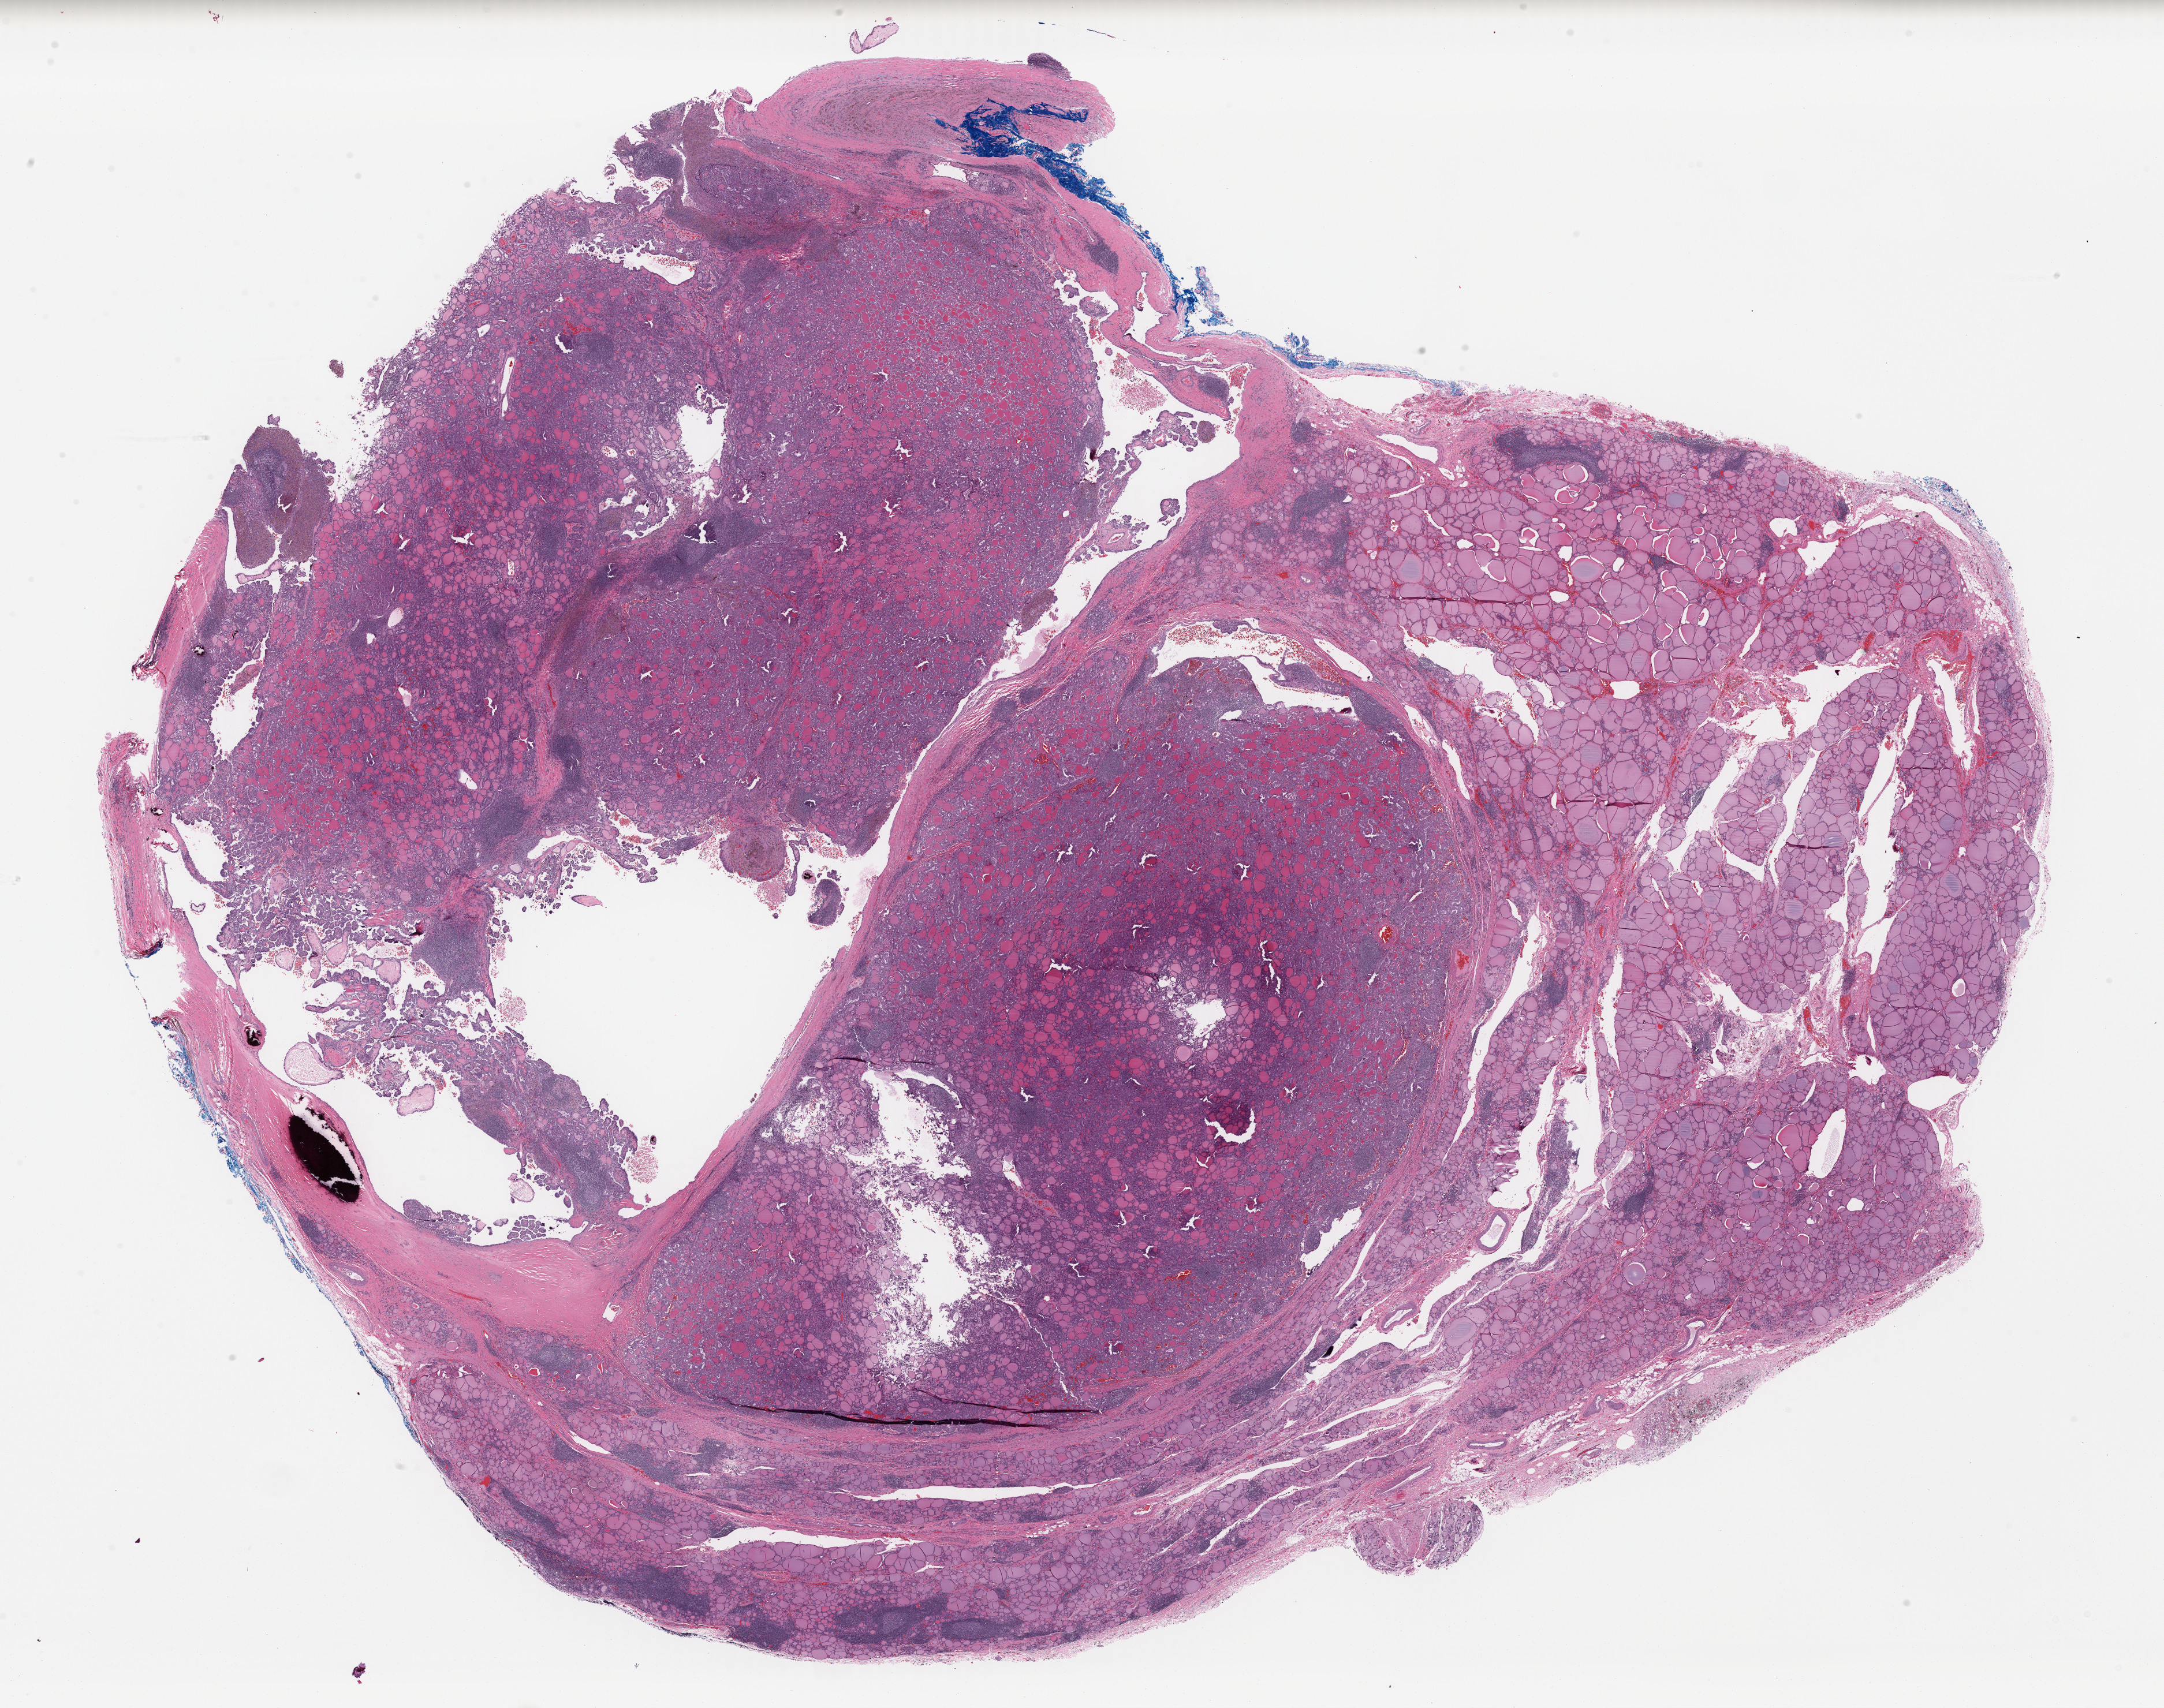
Digitized H&E-stained tissue section (whole slide) — shown as a low-resolution overview of the whole scanned area (about 29.6 x 23.3 mm, slide scanned at 40x). Formalin-fixed paraffin-embedded (FFPE) diagnostic section. Thyroid, primary tumour sample. Female, age 44 years at initial diagnosis.
• laterality: bilateral
• pathologic diagnosis: Papillary adenocarcinoma, NOS (thyroid gland)
• AJCC pathologic stage: I